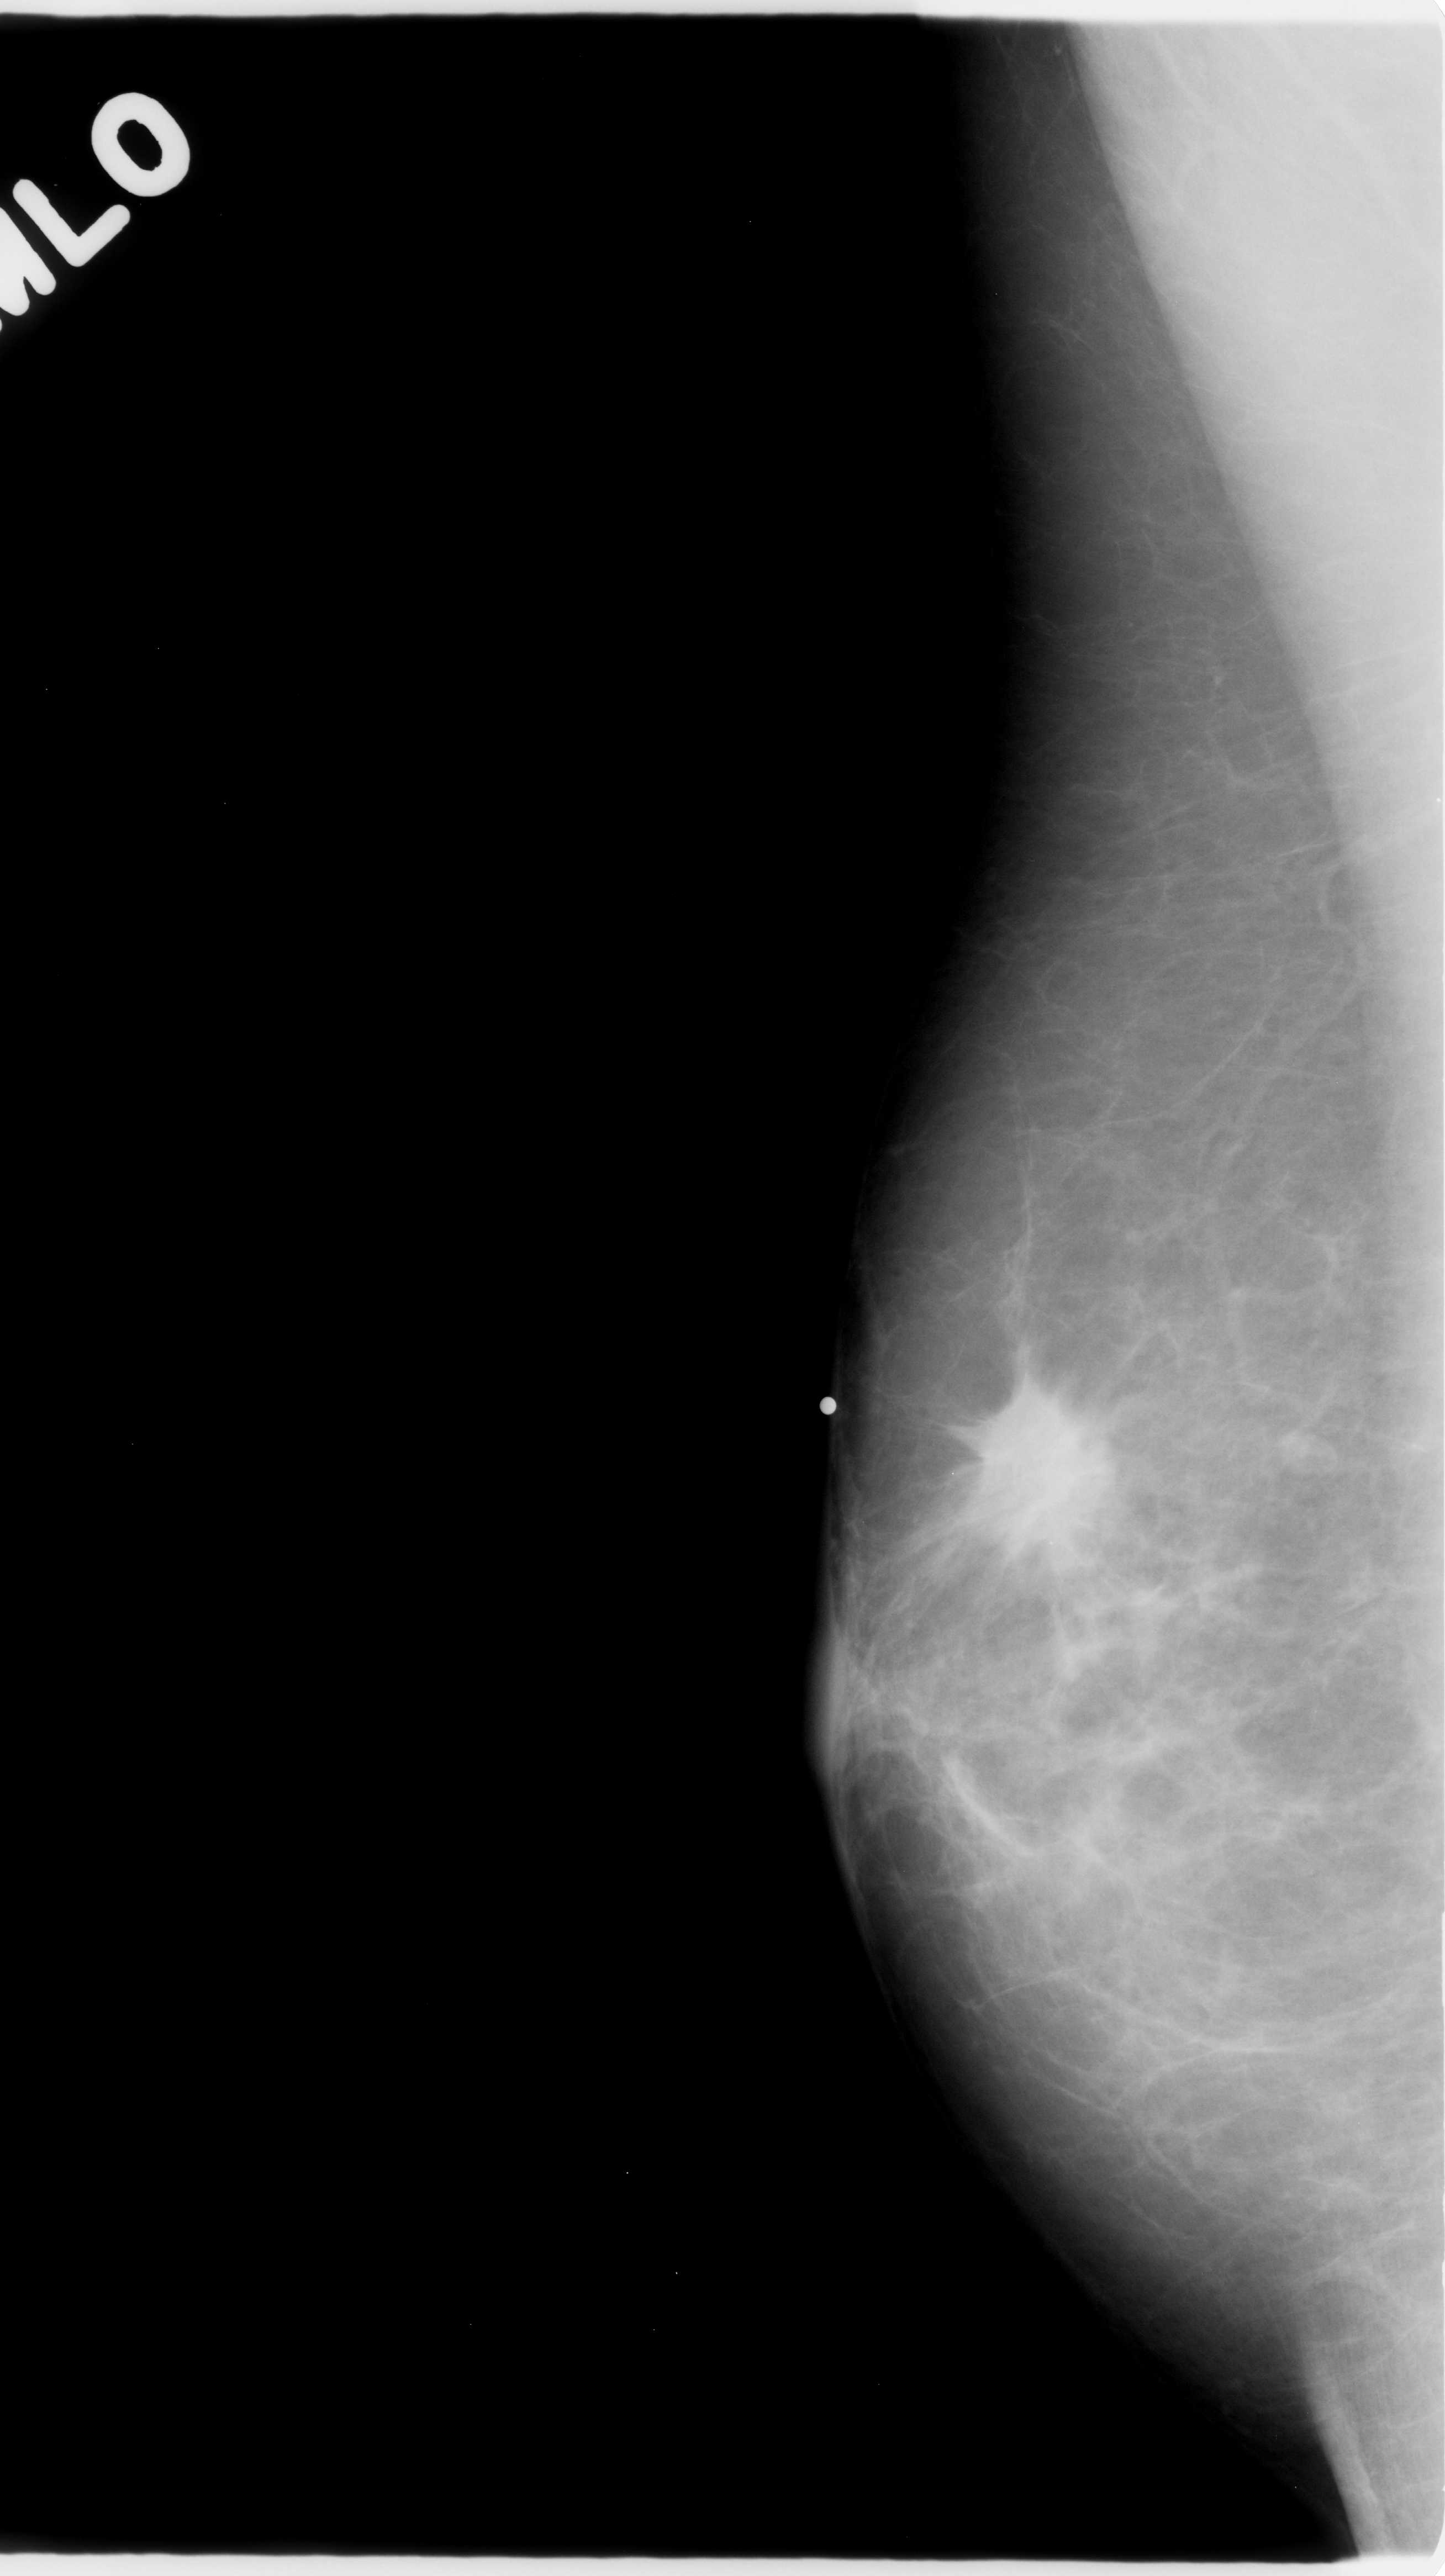
Scanned film-screen mammogram; right breast; MLO view; 1445 × 2576 image matrix.
Expert-marked regions of interest on this film, with their recorded descriptors:
- mass, shape irregular, margins spiculated; BI-RADS assessment category 5; subtlety rating 5 on a 1 (subtle) to 5 (obvious) scale; pathology (as recorded): malignant: bounding box (x1, y1, x2, y2) in pixels: (946, 1345, 1133, 1578)